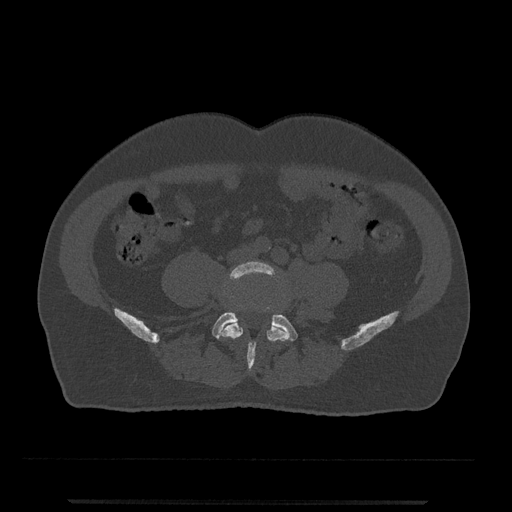
CT including the spine, one axial slice; position 101 of 797 along the scan axis; 120 kVp; bone window (W 1800 / L 400 HU); 0.5 mm slice thickness; 512 × 512 image matrix. Patient: male, 63 years. From the clinical record (not read from this slice): primary cancer: prostate.
Outlined on this slice (semi-automatically segmented with operator editing):
- L4 vertebra: bounding box <220,261,289,369> (left, top, right, bottom; pixels)
- L5 vertebra: <212,307,298,360>